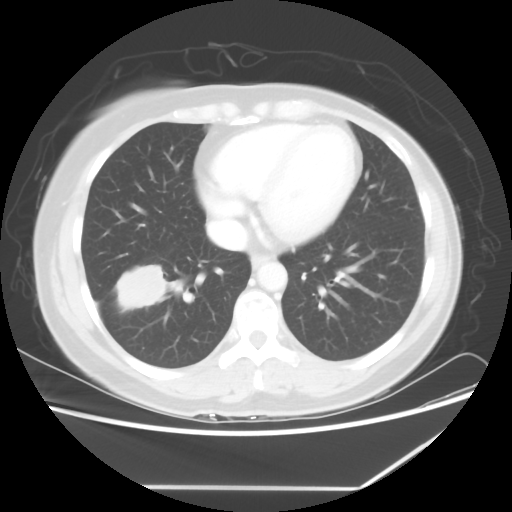
Chest CT, one axial slice; position 23 of 60 along the scan axis; 100 kVp; lung window (W 1500 / L -600 HU); 512 × 512 image matrix, field of view 374 × 374 mm. Female patient, age 42 years. Case-level facts recorded for this patient, not image findings: clinical TNM (as recorded): T2 N1 M0.
Structures marked on this image (rectangle marked by the reading radiologist):
- lung tumour (recorded histology: adenocarcinoma): bounding box (x1, y1, x2, y2) in pixels: (107, 261, 166, 315)